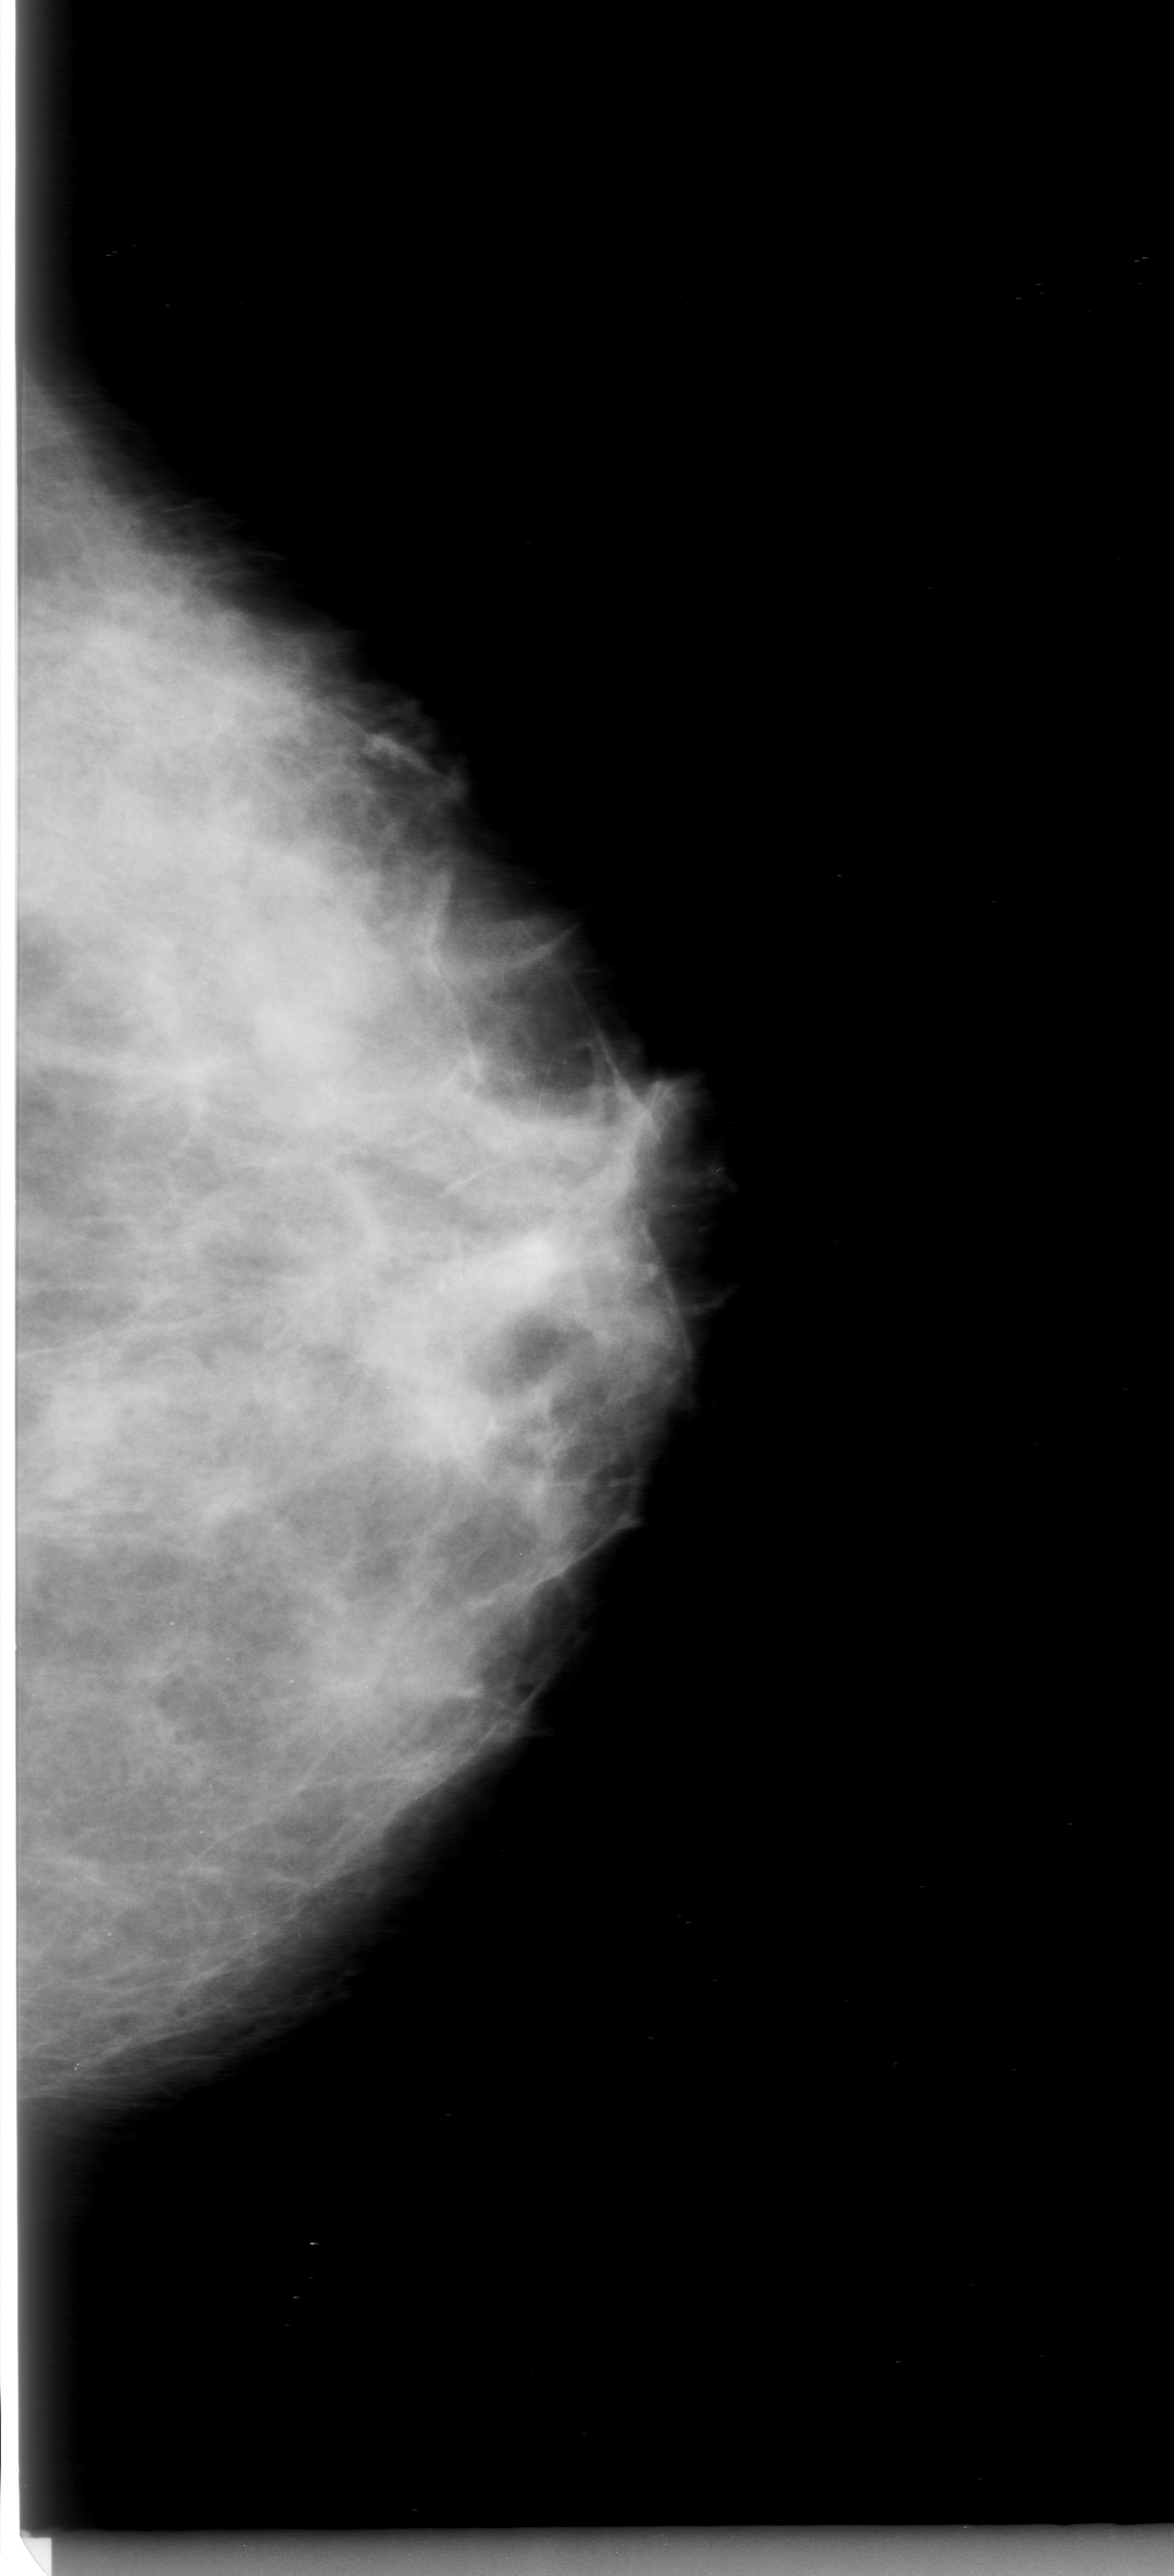
Mammogram (digitized film); left breast; CC view.
- Finding: mass, shape lobulated, margins obscured; BI-RADS assessment category 0; subtlety rating 5 on a 1 (subtle) to 5 (obvious) scale; pathology result (as recorded, not read from the image): benign.